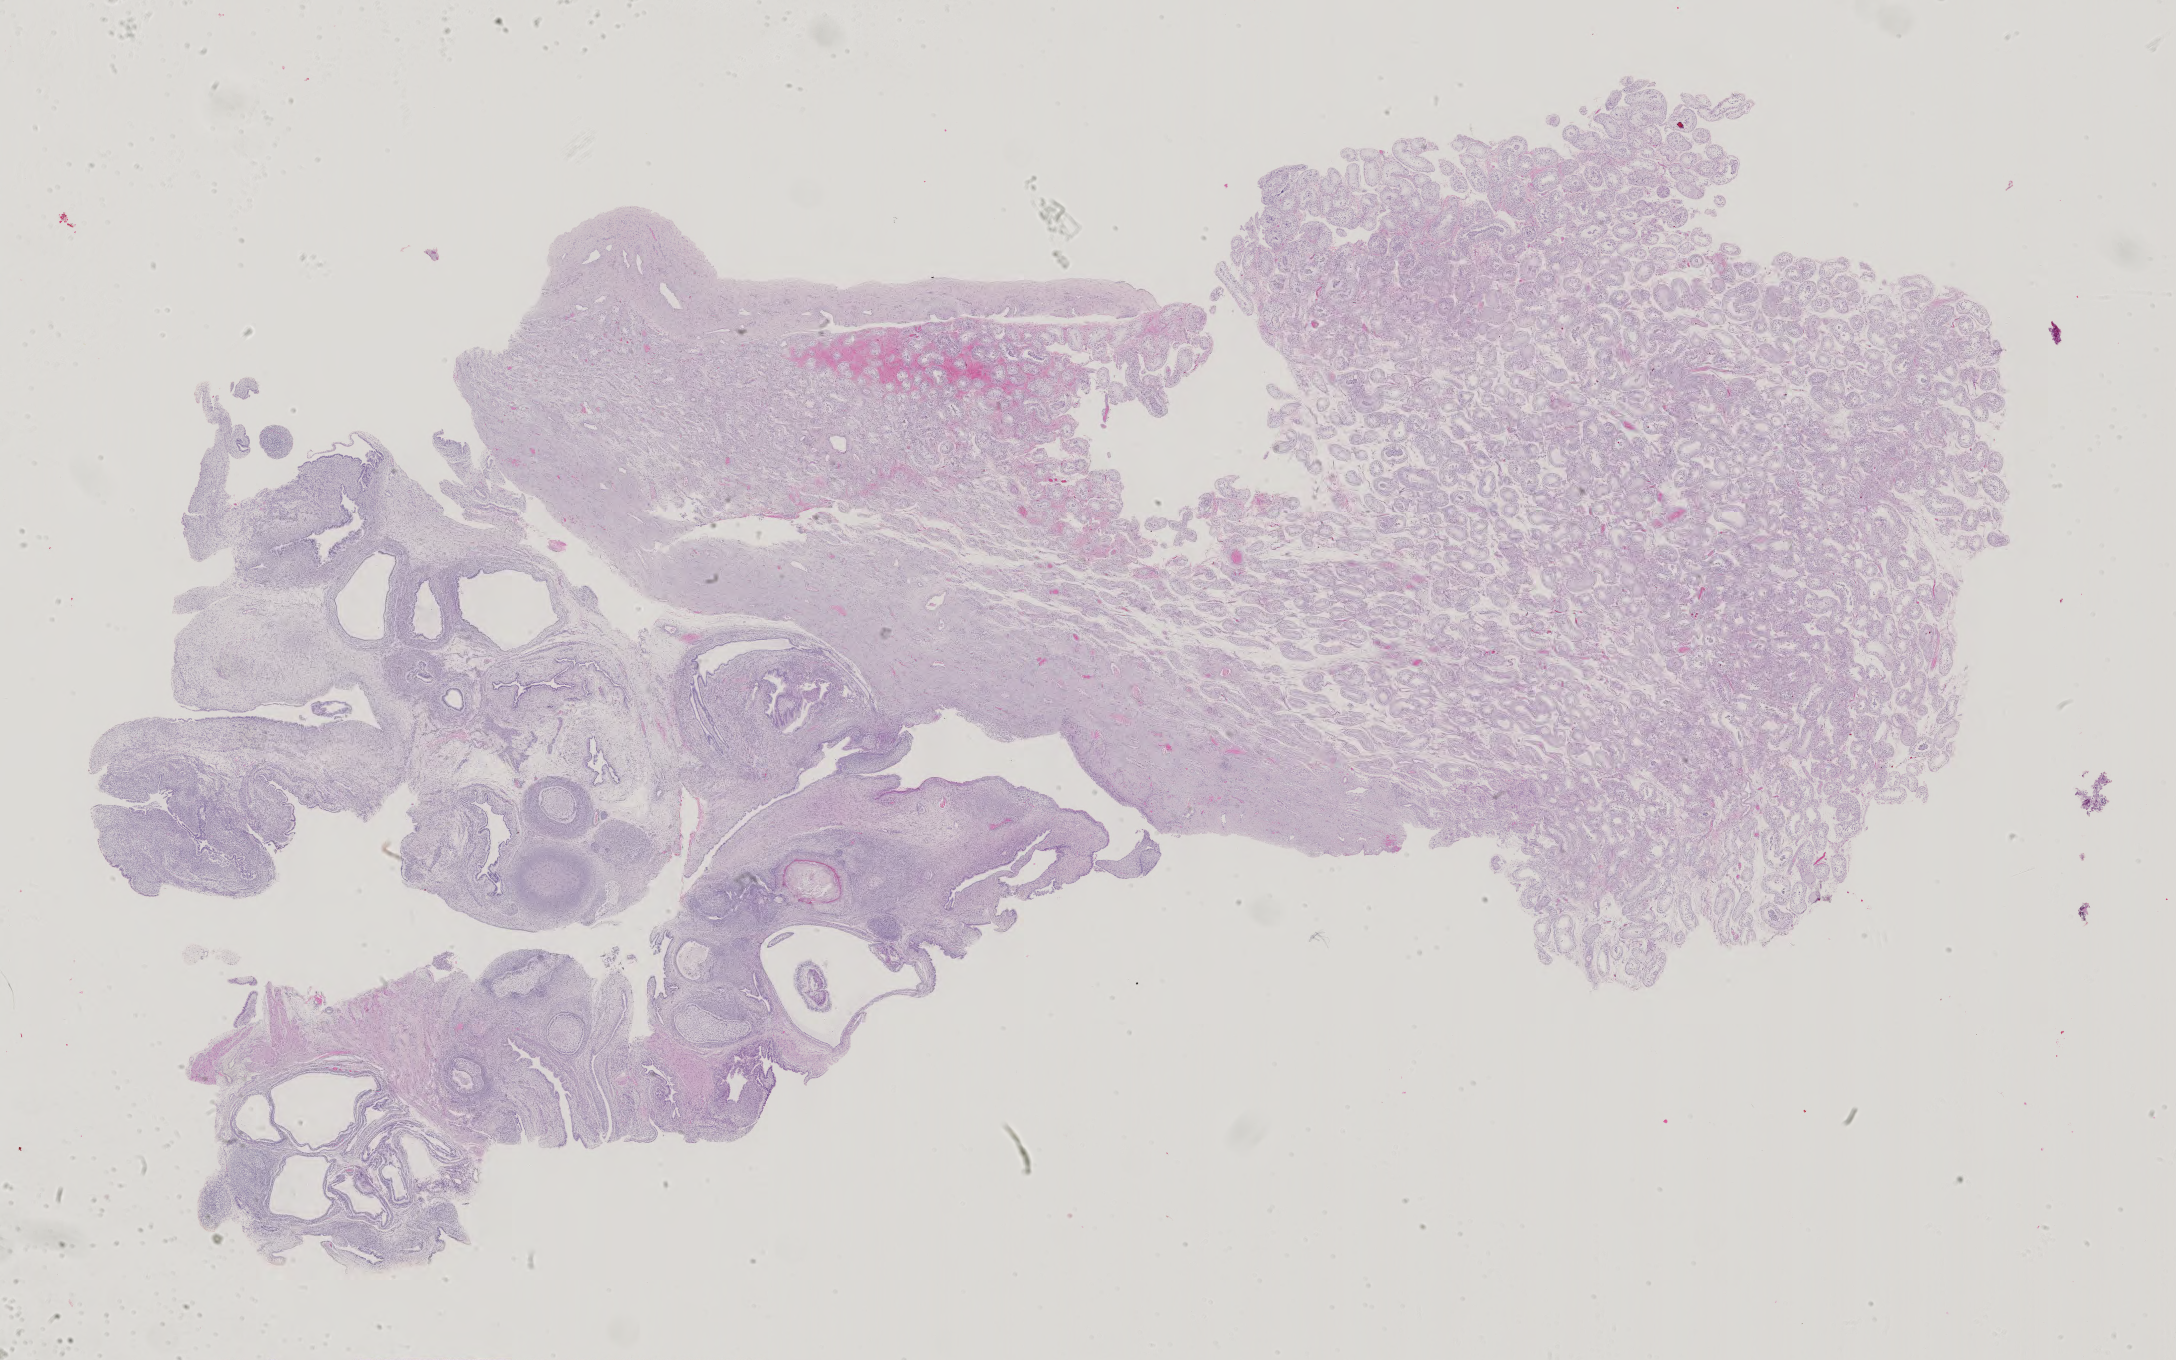
Whole-slide histology image, H&E — shown as a low-resolution overview of the whole scanned area (about 31.7 x 19.8 mm, slide scanned at 40x). Male patient.
Specimen: formalin-fixed paraffin-embedded (FFPE) diagnostic section; testis, primary tumour sample.